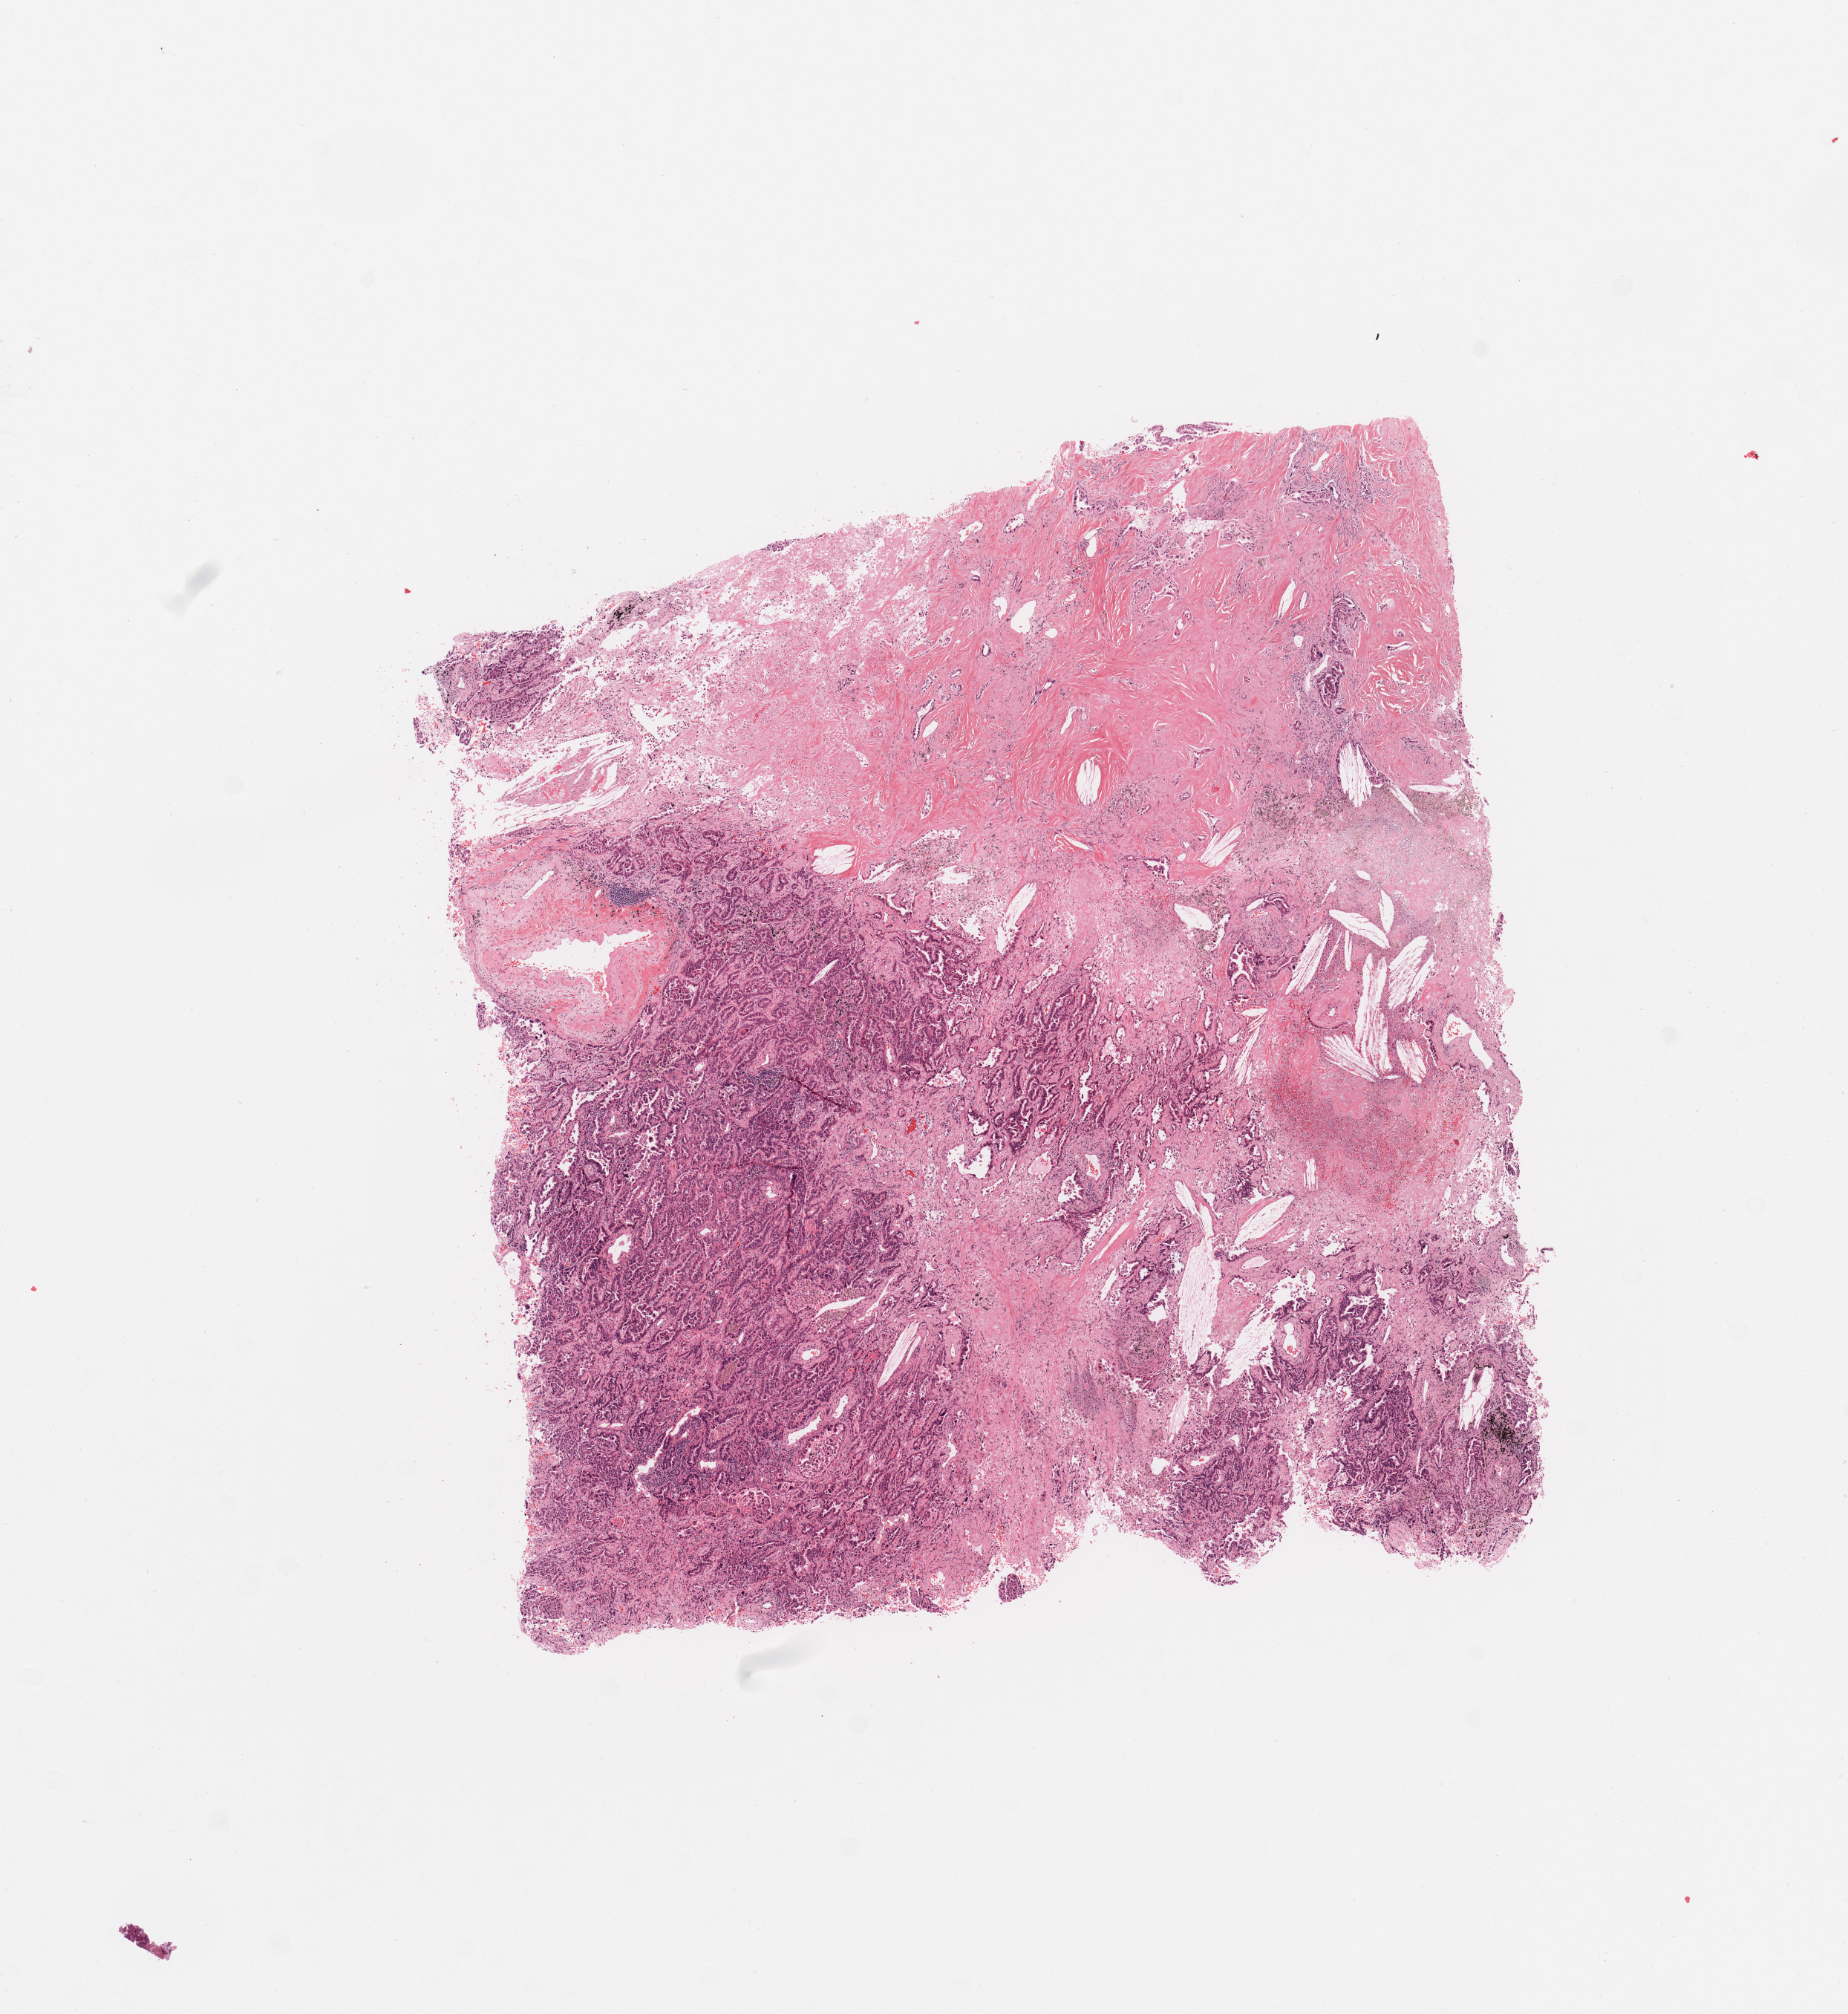
Digitized H&E-stained tissue section (whole slide), whole scanned area (about 9.8 x 10.7 mm) shown as a low-resolution overview, tumour tissue sample, sampled site: lung. 49-year-old male patient. Histologic grade: G3 (poorly differentiated). Pathologist review of this section (percent, as recorded): tumour nuclei 60%, necrosis 15%.
• histologic diagnosis: Adenocarcinoma, NOS
• primary tumour site (as recorded): right lower lobe
• AJCC pathologic stage: IIA